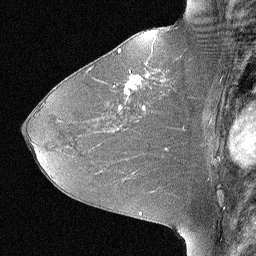
Breast MRI (dynamic contrast-enhanced), one sagittal slice. Slice 38 of 64 in the series (ordered by position). Dynamic contrast-enhanced study with each time point stored as its own series, time point 2 of 3 at this slice position (early post-contrast, ordered by acquisition time). 1.5 T. TE 4 ms, TR 30 ms. 2.25 mm slice thickness. 256 × 256 image matrix. Patient: female, 46 years. From the clinical record (not read from this slice): setting: breast cancer imaged before/during neoadjuvant chemotherapy; receptor status: HR-positive, HER2-negative.
Annotated regions visible in this slice (semi-automatic segmentation, software-assisted and operator-edited):
- analysis volume of interest (the breast-tissue region the enhancement analysis was run in; not a lesion): box from (x=106, y=43) to (x=184, y=119) px
- tumour enhancement mask (voxels above the 90 % enhancement threshold inside the analysis volume of interest): (x=118, y=49)–(x=166, y=95)